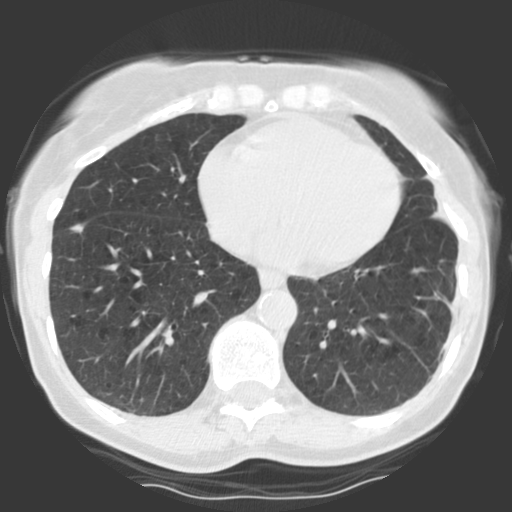
Chest CT (low-dose screening protocol), one axial image. First (baseline) screen. Lung window (W 1500 / L -600 HU). 2.5 mm slice thickness. Slice 43 of 123 in the series. Female participant, aged 68 years at enrolment. Former smoker at enrolment.
• Expert reader's lesion annotation, bounding box [x1, y1, x2, y2] px = [58, 210, 98, 249].
• The screening reader recorded 2 non-calcified nodules or masses ≥4 mm on this exam (right lower lobe, right middle lobe); which of them this box marks is not recorded.